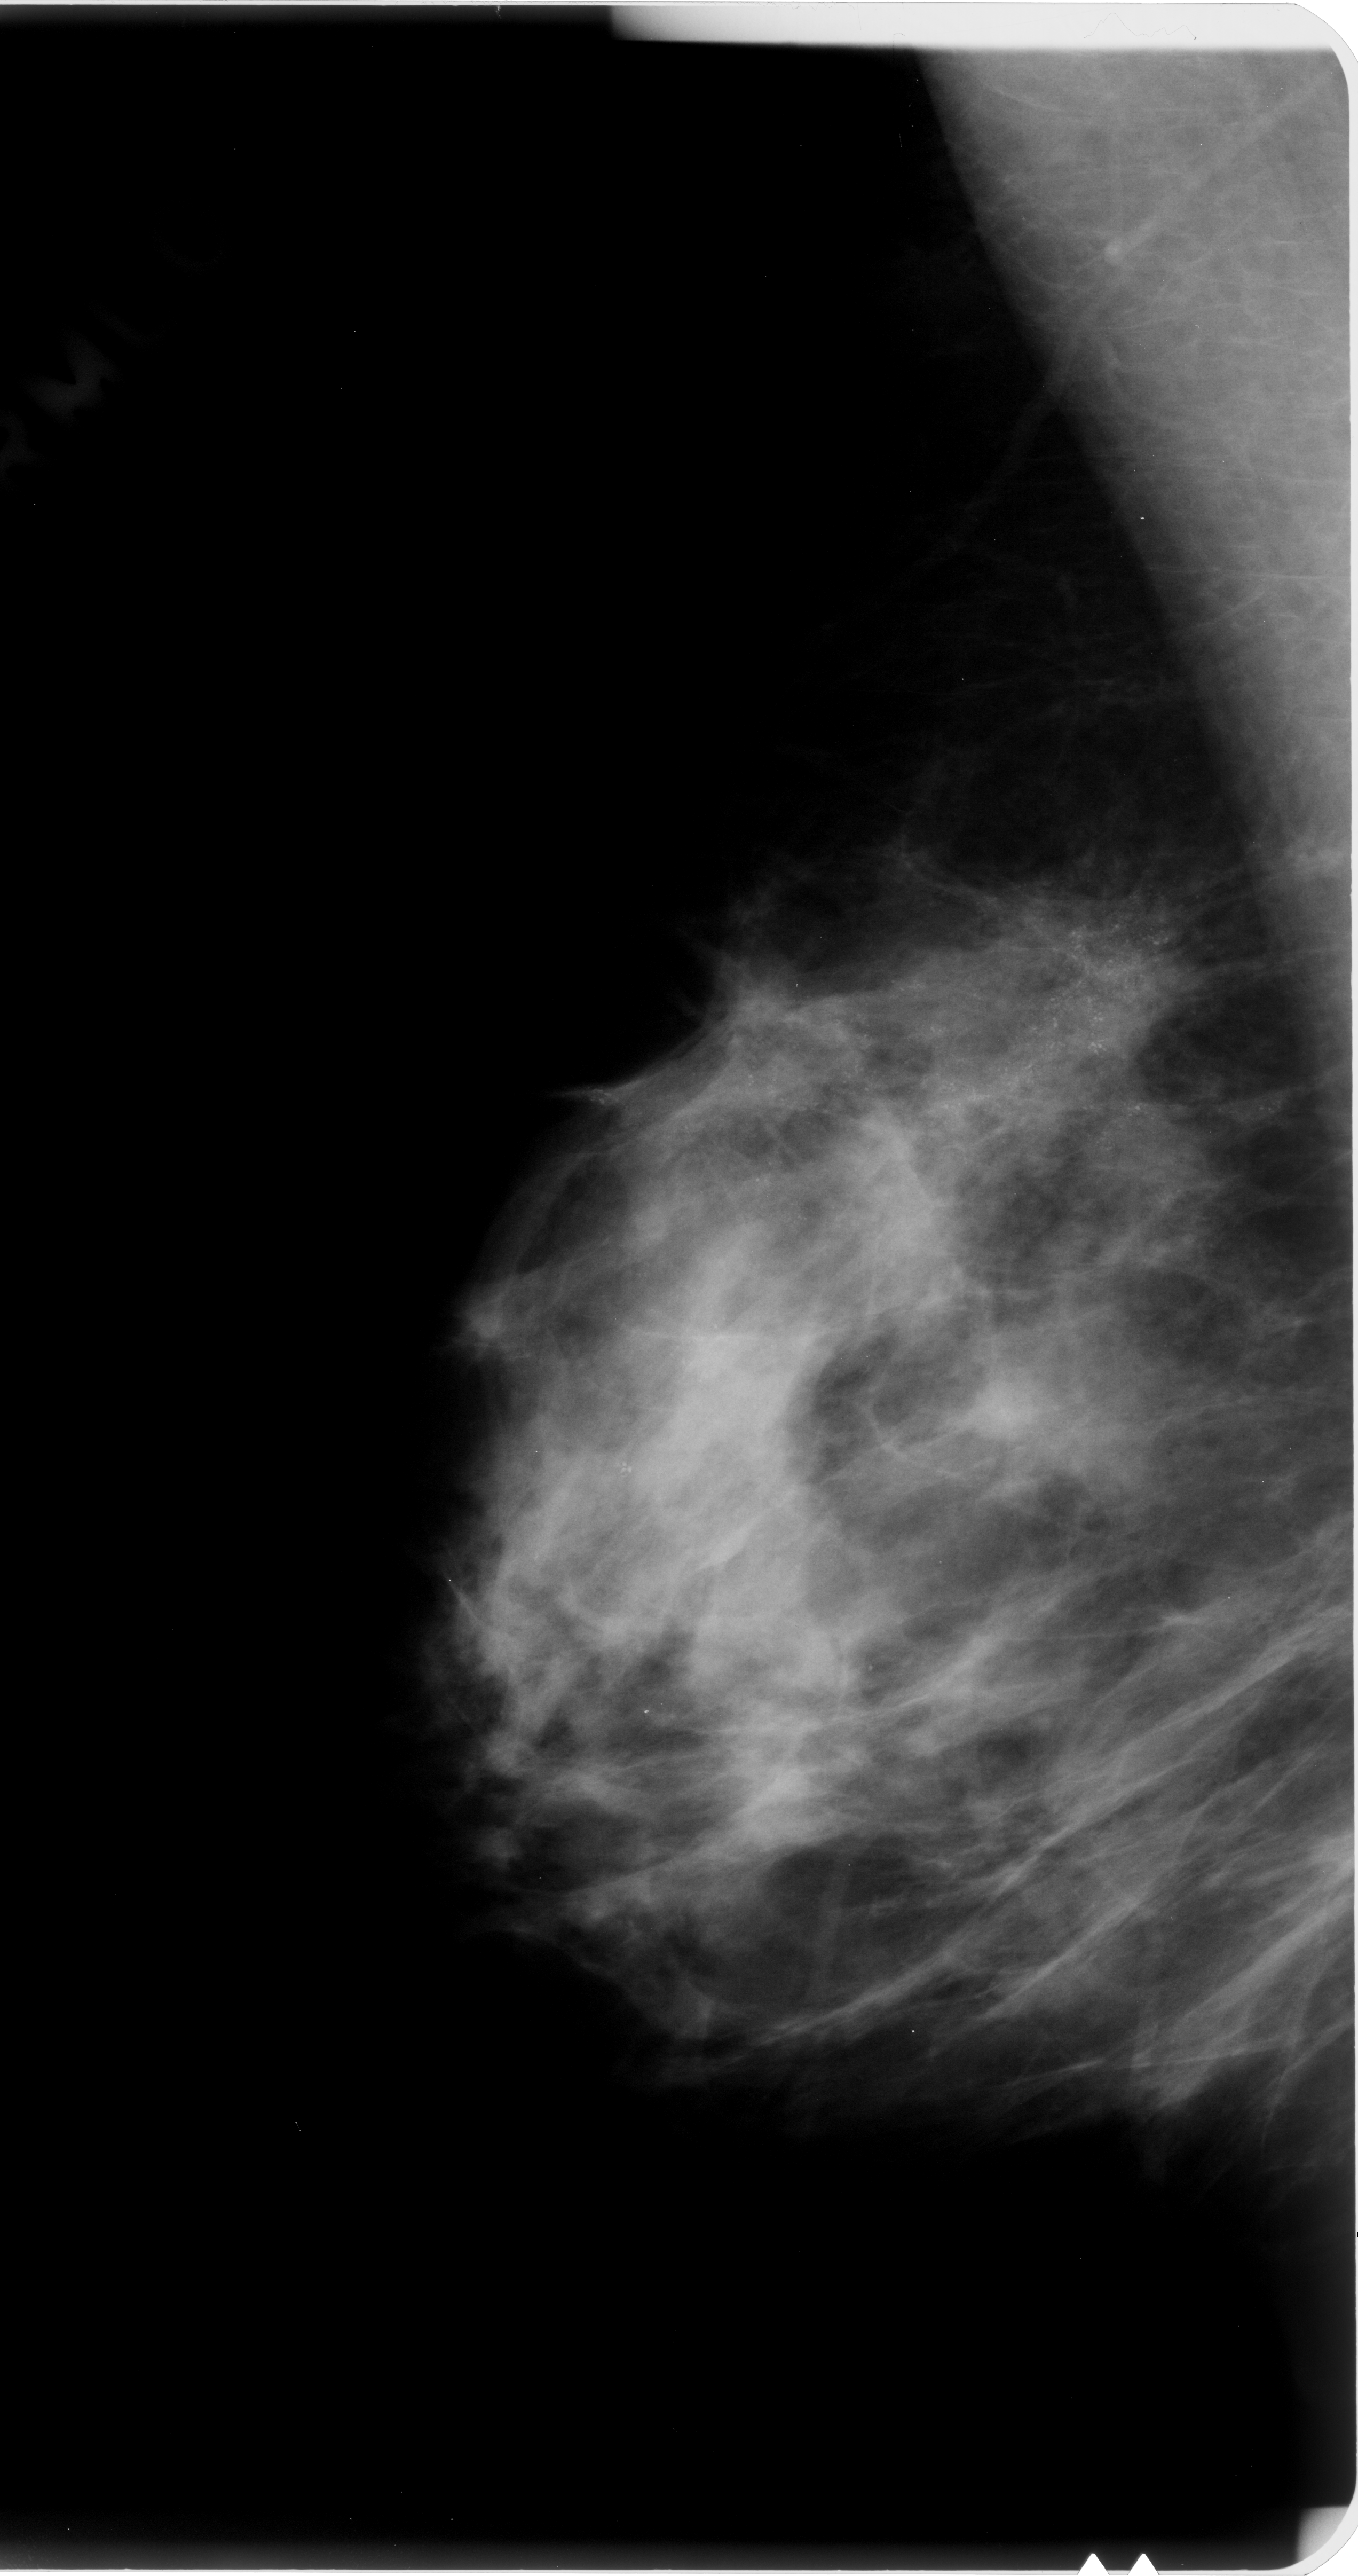
Mammogram (digitized film); right breast; mediolateral oblique (MLO) view; BI-RADS breast density category 3 (scale 1–4).
- Calcifications, morphology pleomorphic, distribution regional; BI-RADS assessment category 5; subtlety rating 5 on a 1 (subtle) to 5 (obvious) scale; pathology (as recorded): malignant.